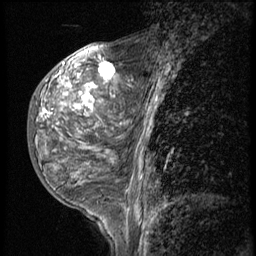
Breast MRI (dynamic contrast-enhanced), one sagittal slice. Slice 20 of 56 in the series (ordered by position). 3 images stored at this slice position (order not interpretable as contrast timing). 1.5 T. TE 4.2 ms, TR 9 ms. 2.5 mm slice thickness. 256 × 256 image matrix, field of view 180 × 180 mm. Patient: female, 50 years. From the clinical record (not read from this slice): setting: breast cancer imaged before/during neoadjuvant chemotherapy; receptor status: triple-negative.
Annotated regions visible in this slice (semi-automatic segmentation, software-assisted and operator-edited):
- analysis volume of interest (the breast-tissue region the enhancement analysis was run in; not a lesion): bounding box (x1, y1, x2, y2) in pixels: (27, 50, 117, 191)
- tumour enhancement mask (voxels above the 140 % enhancement threshold inside the analysis volume of interest): (43, 62, 113, 118)